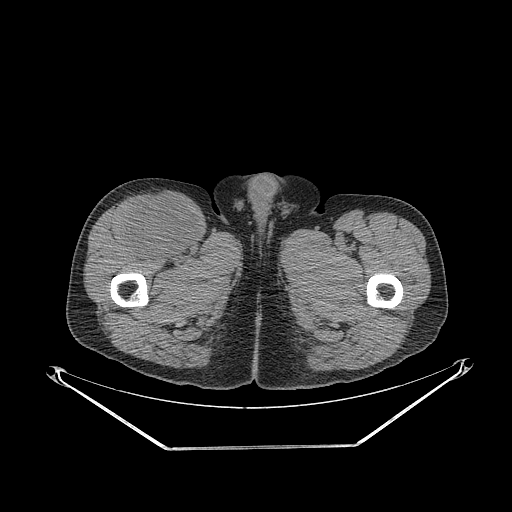
CT of an extremity soft-tissue mass (from a PET/CT study), one axial slice; reconstruction kernel STANDARD; 140 kVp; soft-tissue window (W 400 / L 40 HU); 3.75 mm slice thickness; 512 × 512 image matrix, field of view 500 × 500 mm. Male patient. Case-level facts recorded for this patient, not image findings: histological type: pleiomorphic leiomyosarcoma; grade: intermediate; site of the primary tumour: right thigh.
Outlined on this slice (expert contour drawn on MRI and transferred to this co-registered scan by the dataset authors):
- gross tumour volume including surrounding oedema: box from (x=123, y=194) to (x=200, y=259) px
- gross tumour volume (mass): (x=126, y=194)–(x=200, y=259)